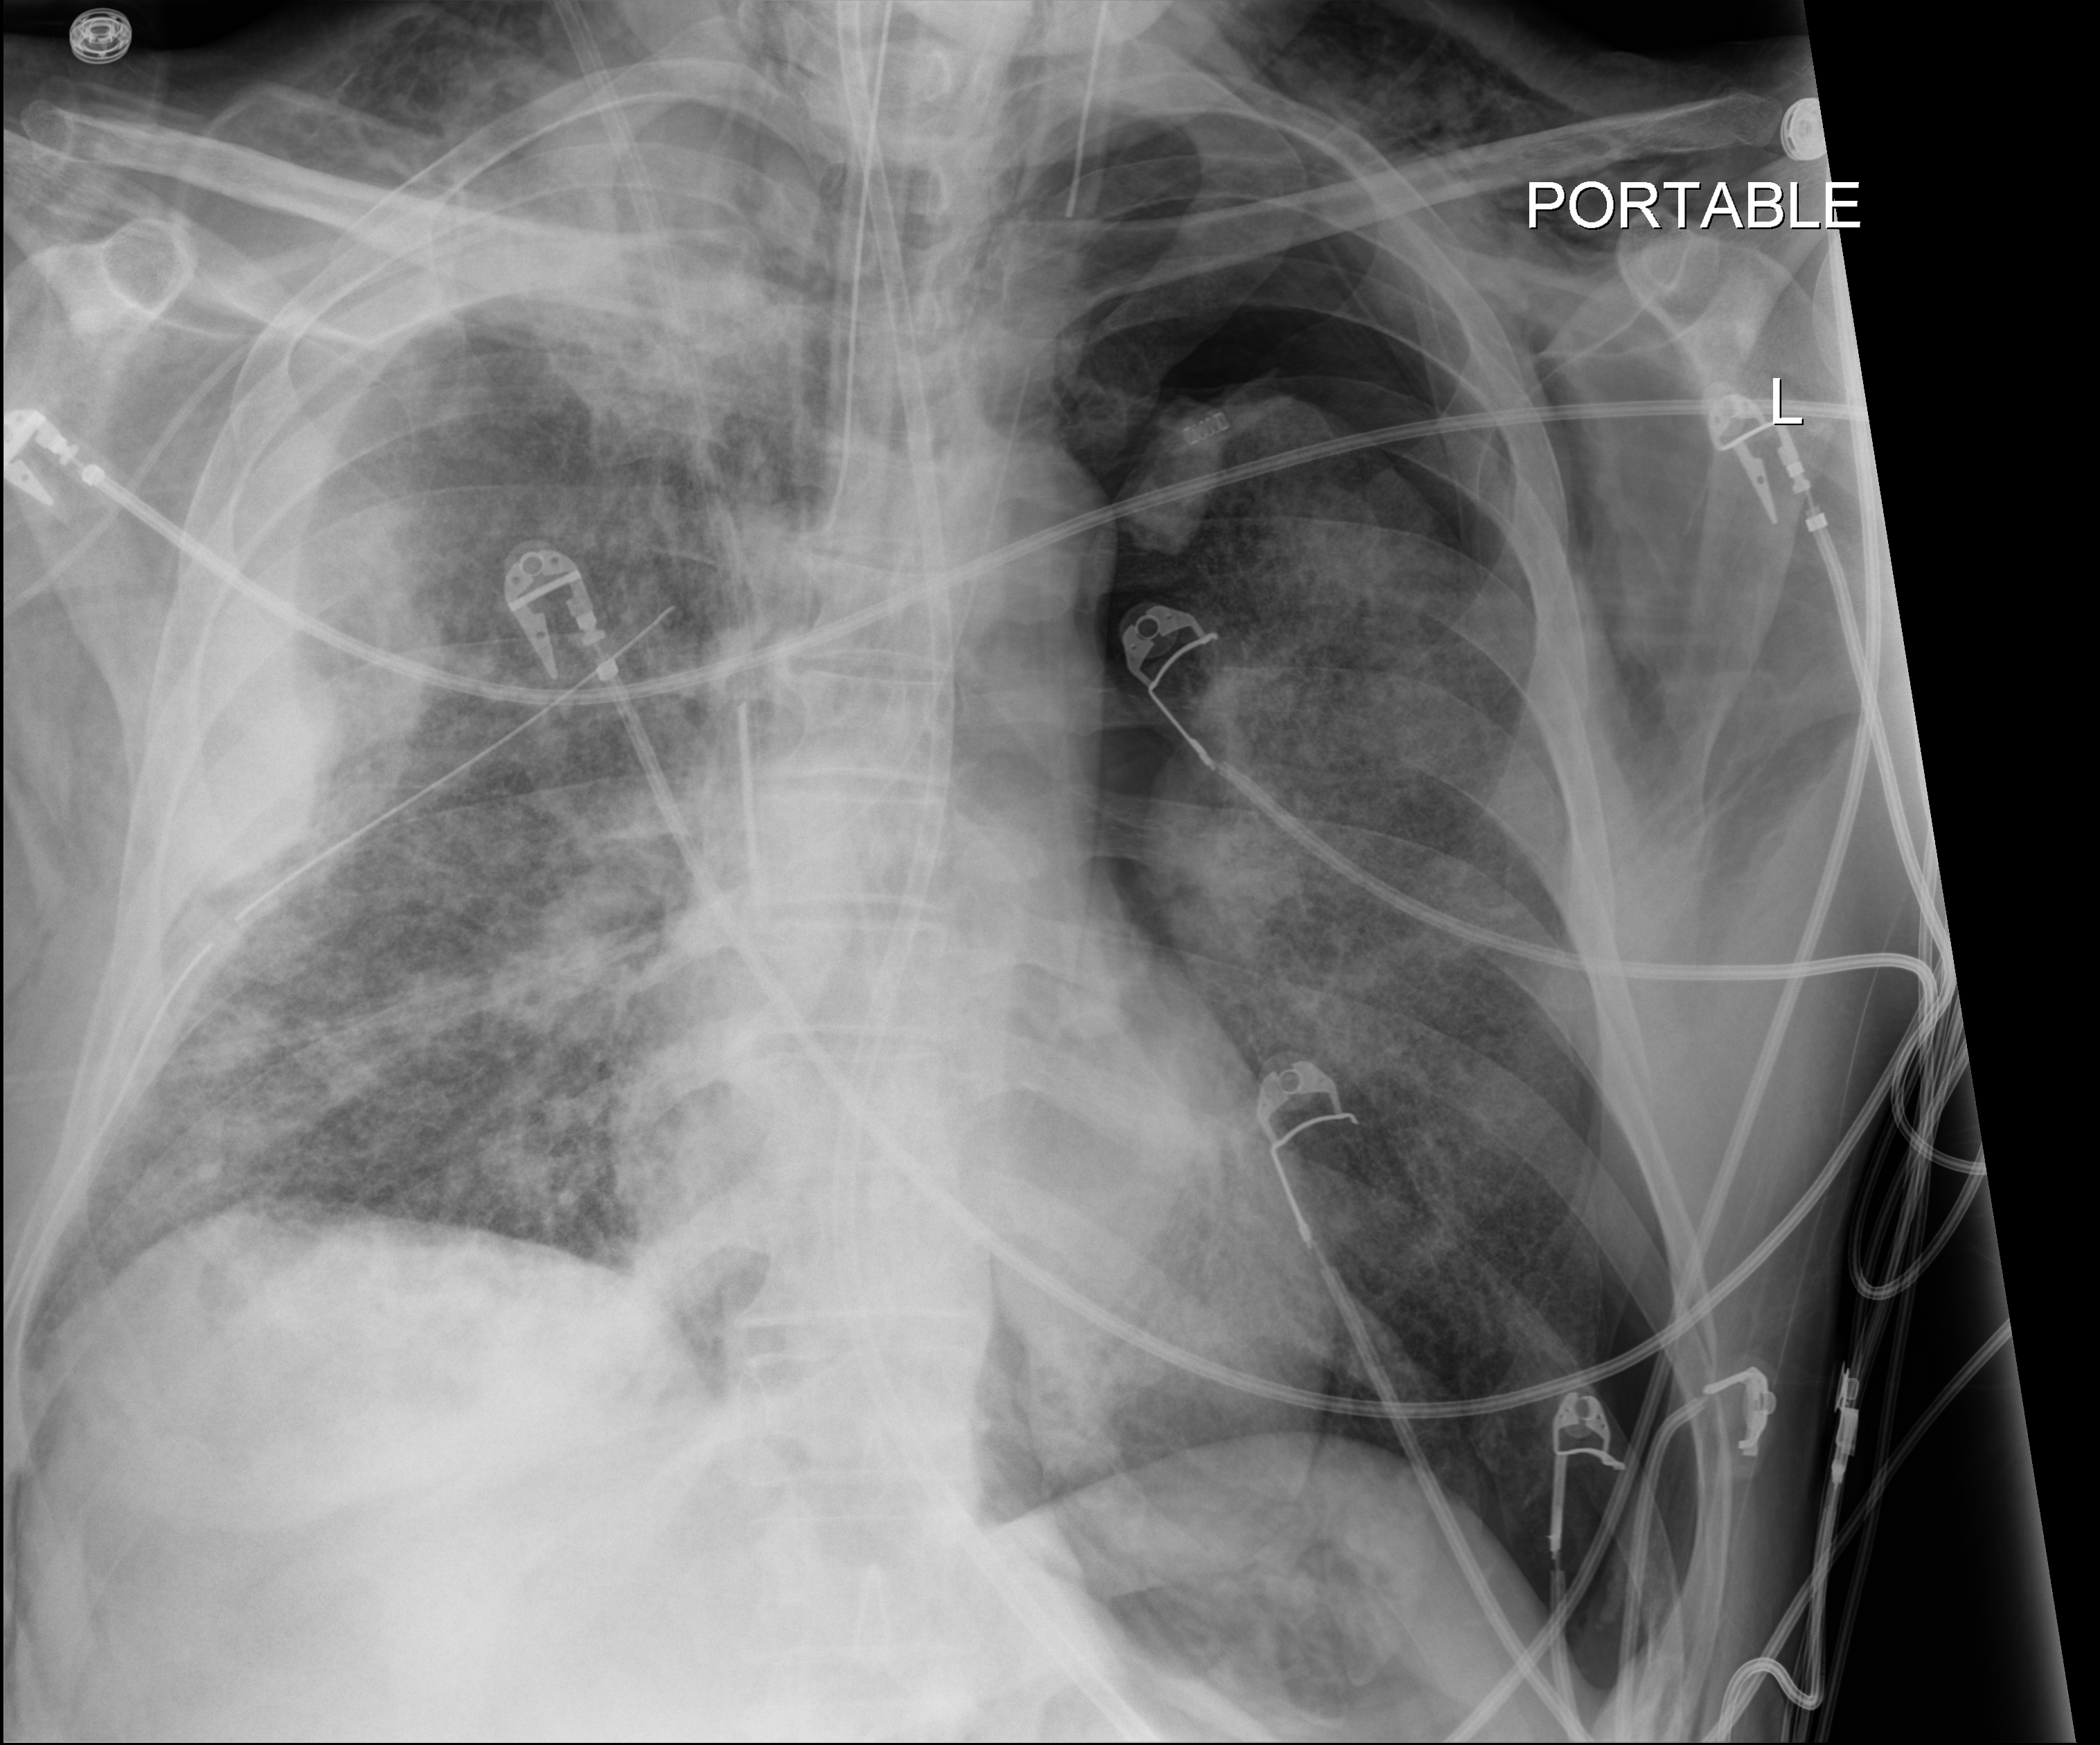
Chest X-ray (portable), anteroposterior (AP) projection. Patient hospitalised with COVID-19; male, aged 18–59 years.
Admission-level facts for this patient (not findings on this image; timing relative to this image not recorded): length of hospital stay: 42 days; mechanically ventilated during this hospital stay: yes.